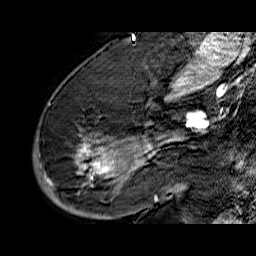
Breast MRI (dynamic contrast-enhanced), one sagittal slice; slice 40 of 60 in the series (ordered by position); dynamic contrast-enhanced series, time point 2 of 6 at this slice position (early post-contrast); 1.5 T; TE 6.5 ms, TR 32.9 ms; 256 × 256 image matrix, field of view 200 × 200 mm. Female patient. Case-level facts recorded for this patient, not image findings: setting: breast cancer imaged before/during neoadjuvant chemotherapy; receptor status: HR-positive, HER2-negative.
Outlined on this slice (semi-automatically segmented with operator editing):
- analysis volume of interest (the breast-tissue region the enhancement analysis was run in; not a lesion): bounding box [x1, y1, x2, y2] px = [33, 74, 176, 210]
- tumour enhancement mask (voxels above the 100 % enhancement threshold inside the analysis volume of interest): [40, 138, 176, 202]